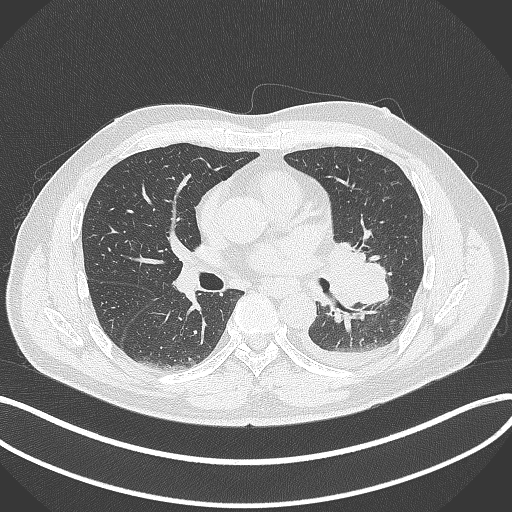
Chest CT, one axial slice; position 189 of 342 along the scan axis; 120 kVp; lung window (W 1500 / L -600 HU); 512 × 512 image matrix. Male patient, age 58 years. Case-level facts recorded for this patient, not image findings: clinical TNM (as recorded): T3 N1 M1b; histopathological grade: G3.
Structures marked on this image (rectangle marked by the reading radiologist):
- lung tumour (recorded histology: small cell carcinoma): bounding box [x1, y1, x2, y2] px = [327, 236, 391, 311]